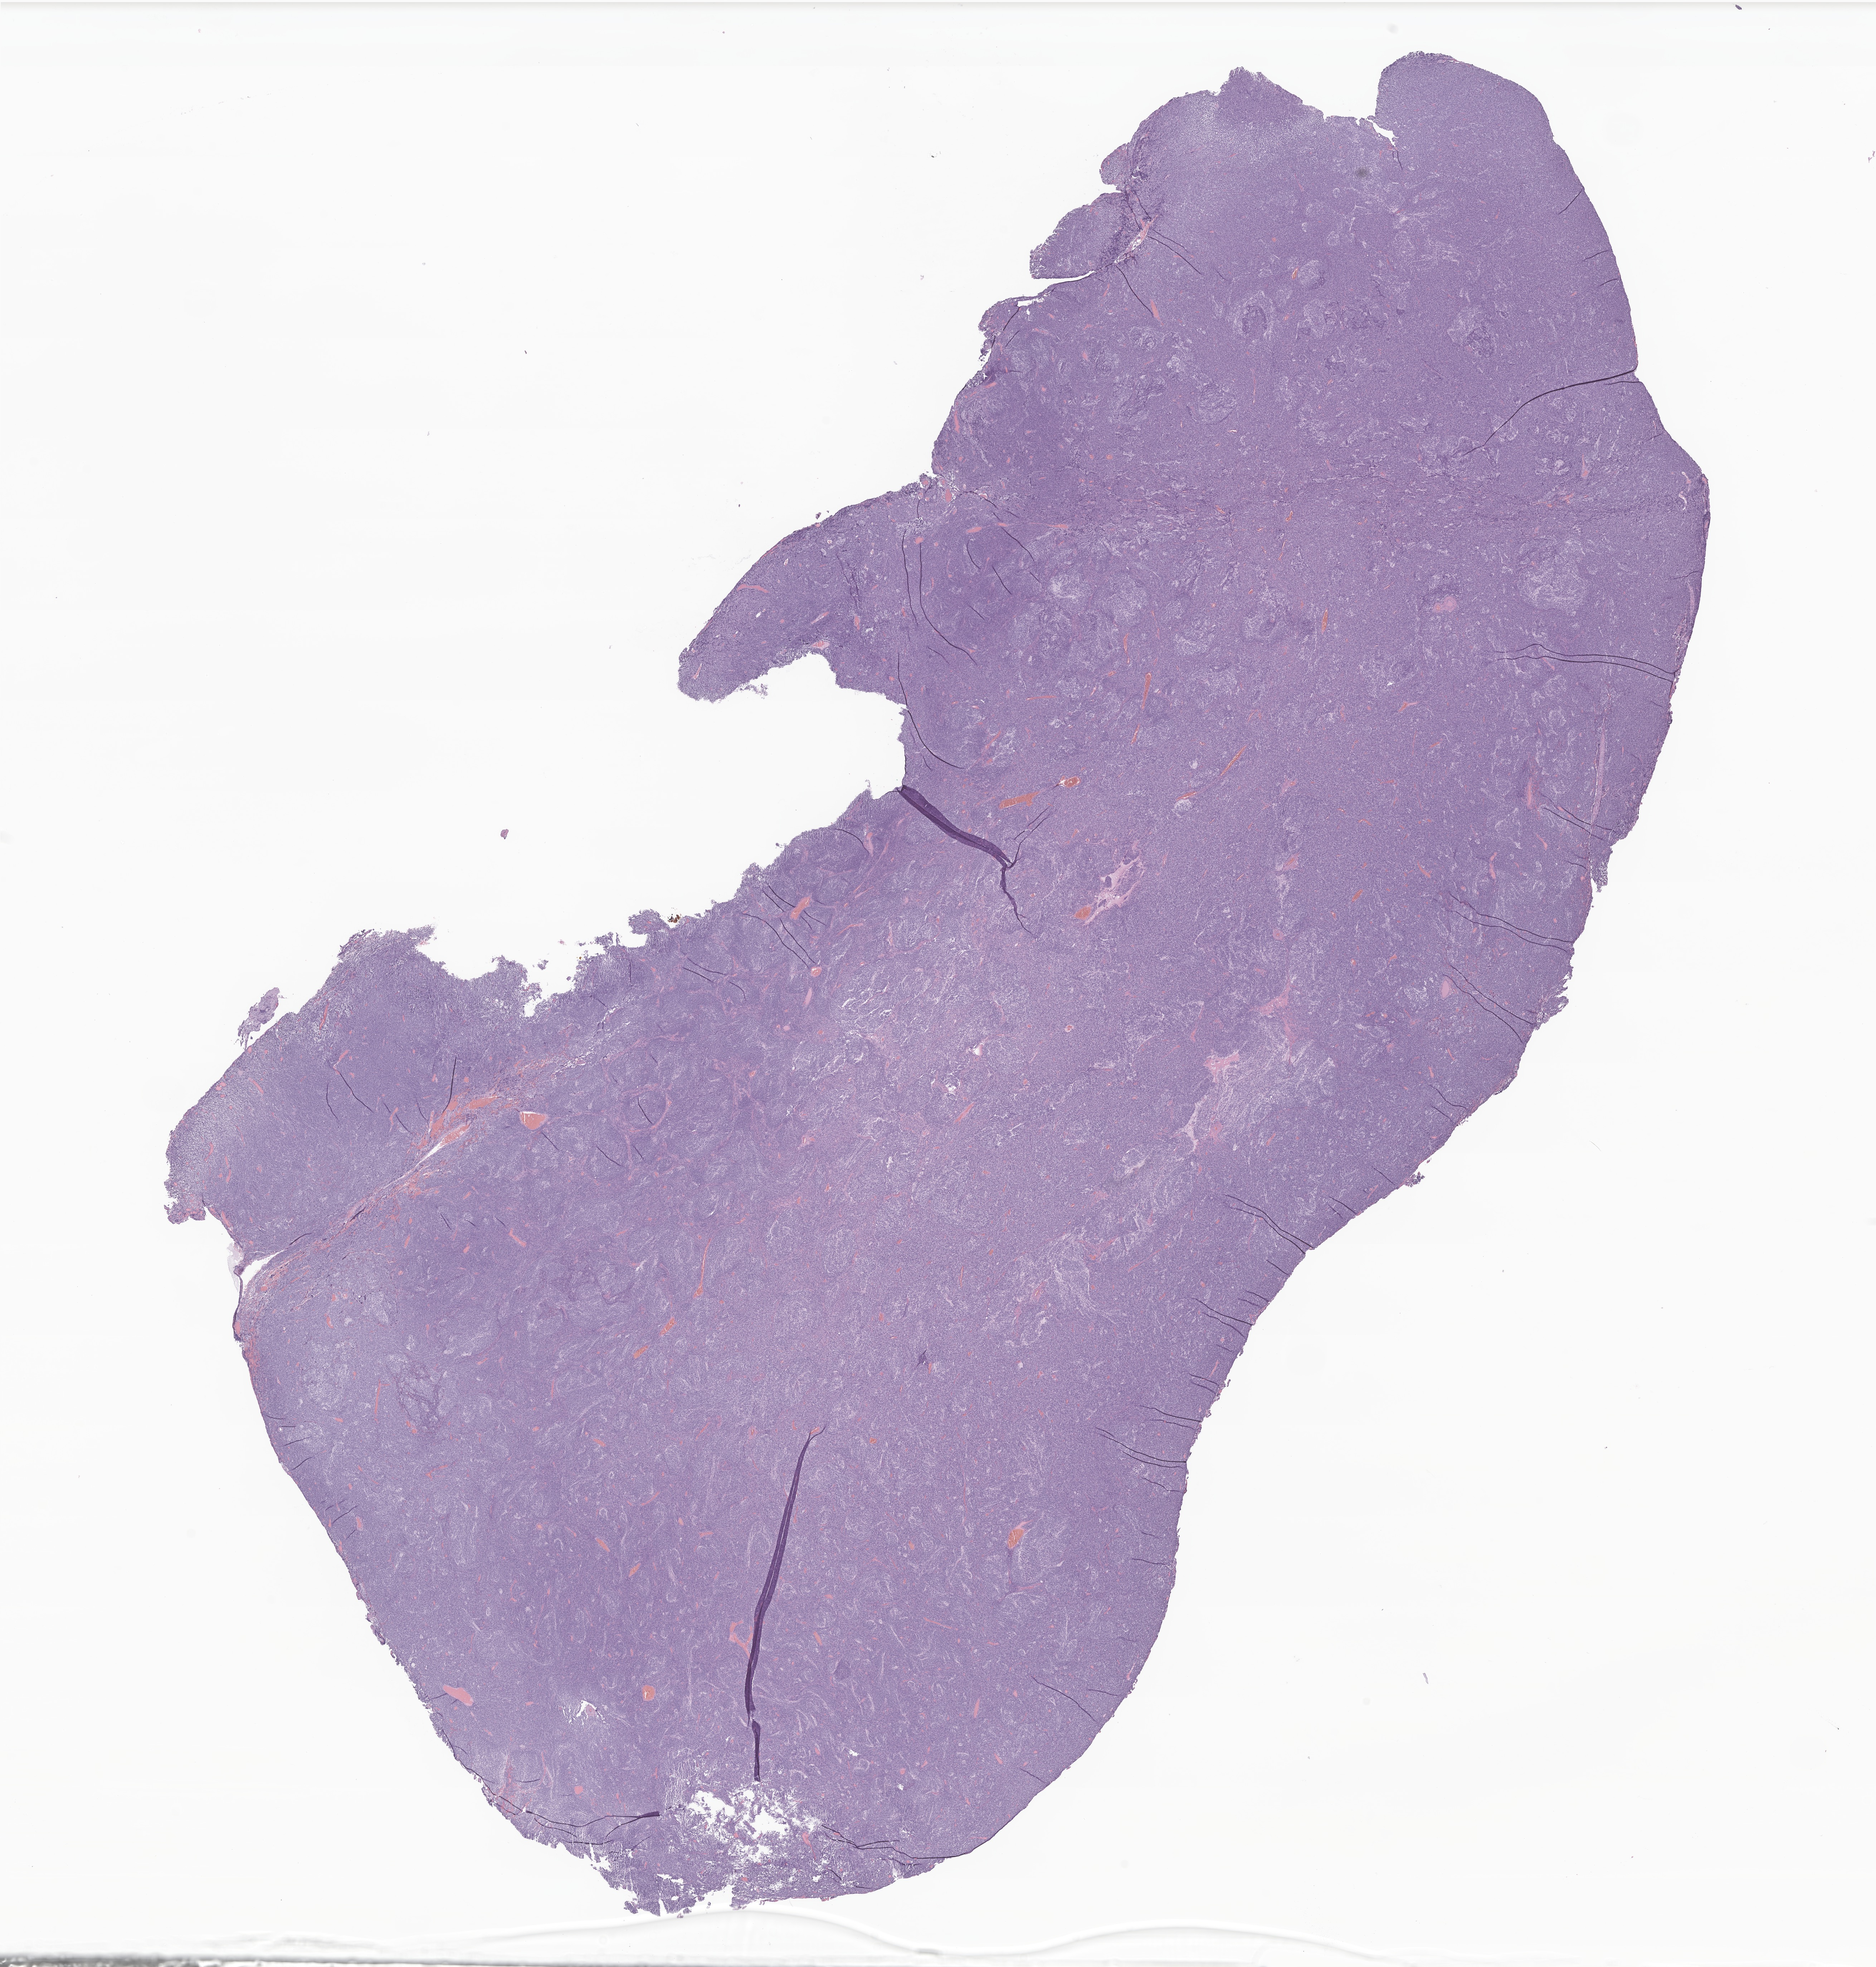
Whole-slide image, haematoxylin and eosin stain of tumor tissue from the brain, shown as a low-resolution overview of the whole scanned area (about 22.1 x 23.2 mm), FFPE section. Female patient, age 545 days (about 1.5 years).
Diagnosis: Glioma, malignant.